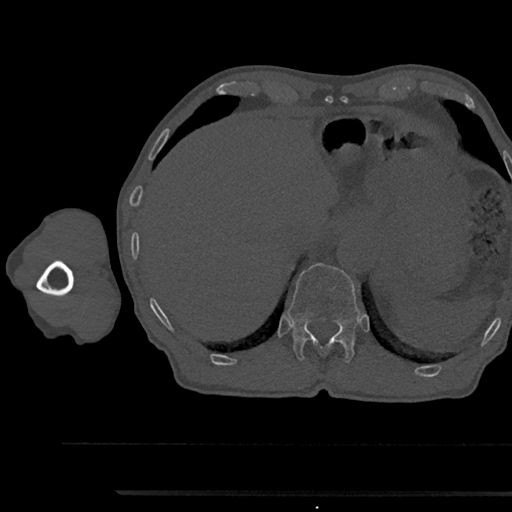
CT including the spine, one axial slice; slice 735 of 797 in the series (ordered by position); bone window (W 1800 / L 400 HU); 512 × 512 image matrix. Male patient, age 79 years. Case-level facts recorded for this patient, not image findings: primary cancer: prostate.
Structures marked on this image (semi-automatically segmented with operator editing):
- T12 vertebra: bounding box (x1, y1, x2, y2) in pixels: (287, 263, 359, 363)